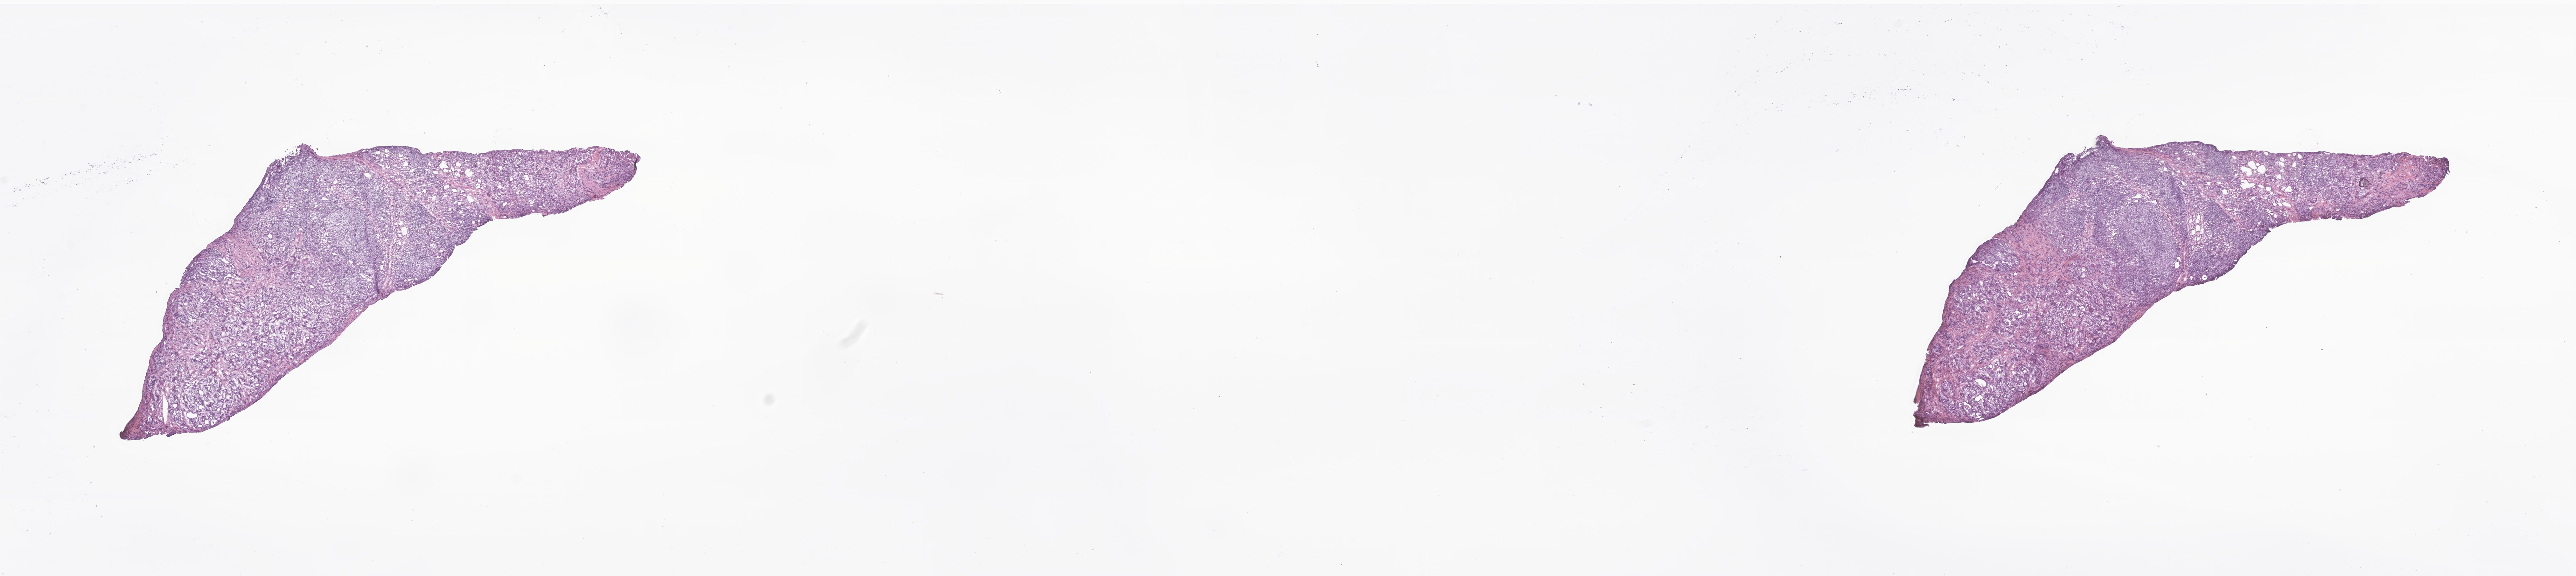
Whole-slide image, hematoxylin and eosin (H&E) stain of tumor tissue from the thyroid, shown as a low-resolution overview of the whole scanned area (about 34.1 x 7.6 mm), frozen section (OCT-embedded). Patient: male, age 186 months (15 years 6 months).
Diagnosis: Papillary carcinoma, NOS.